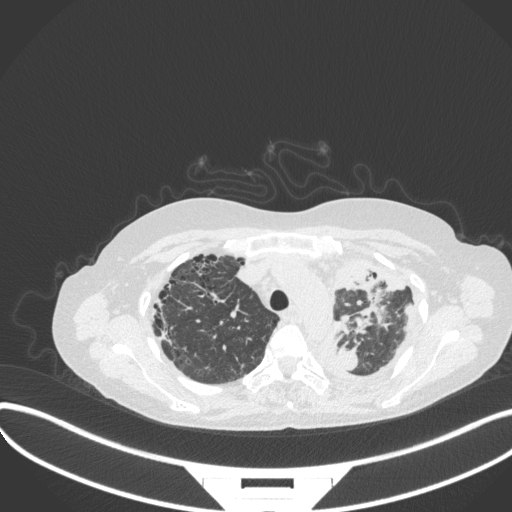
Chest CT, one axial slice; position 264 of 373 along the scan axis; reconstruction kernel B31f; lung window (W 1500 / L -600 HU); 1 mm slice thickness; 512 × 512 image matrix, field of view 400 × 400 mm. Female patient, age 56 years. Case-level facts recorded for this patient, not image findings: clinical TNM (as recorded): T1 N0 M0.
Annotated regions visible in this slice (bounding box drawn by a radiologist):
- lung tumour (recorded histology: adenocarcinoma): box from (x=337, y=257) to (x=405, y=329) px